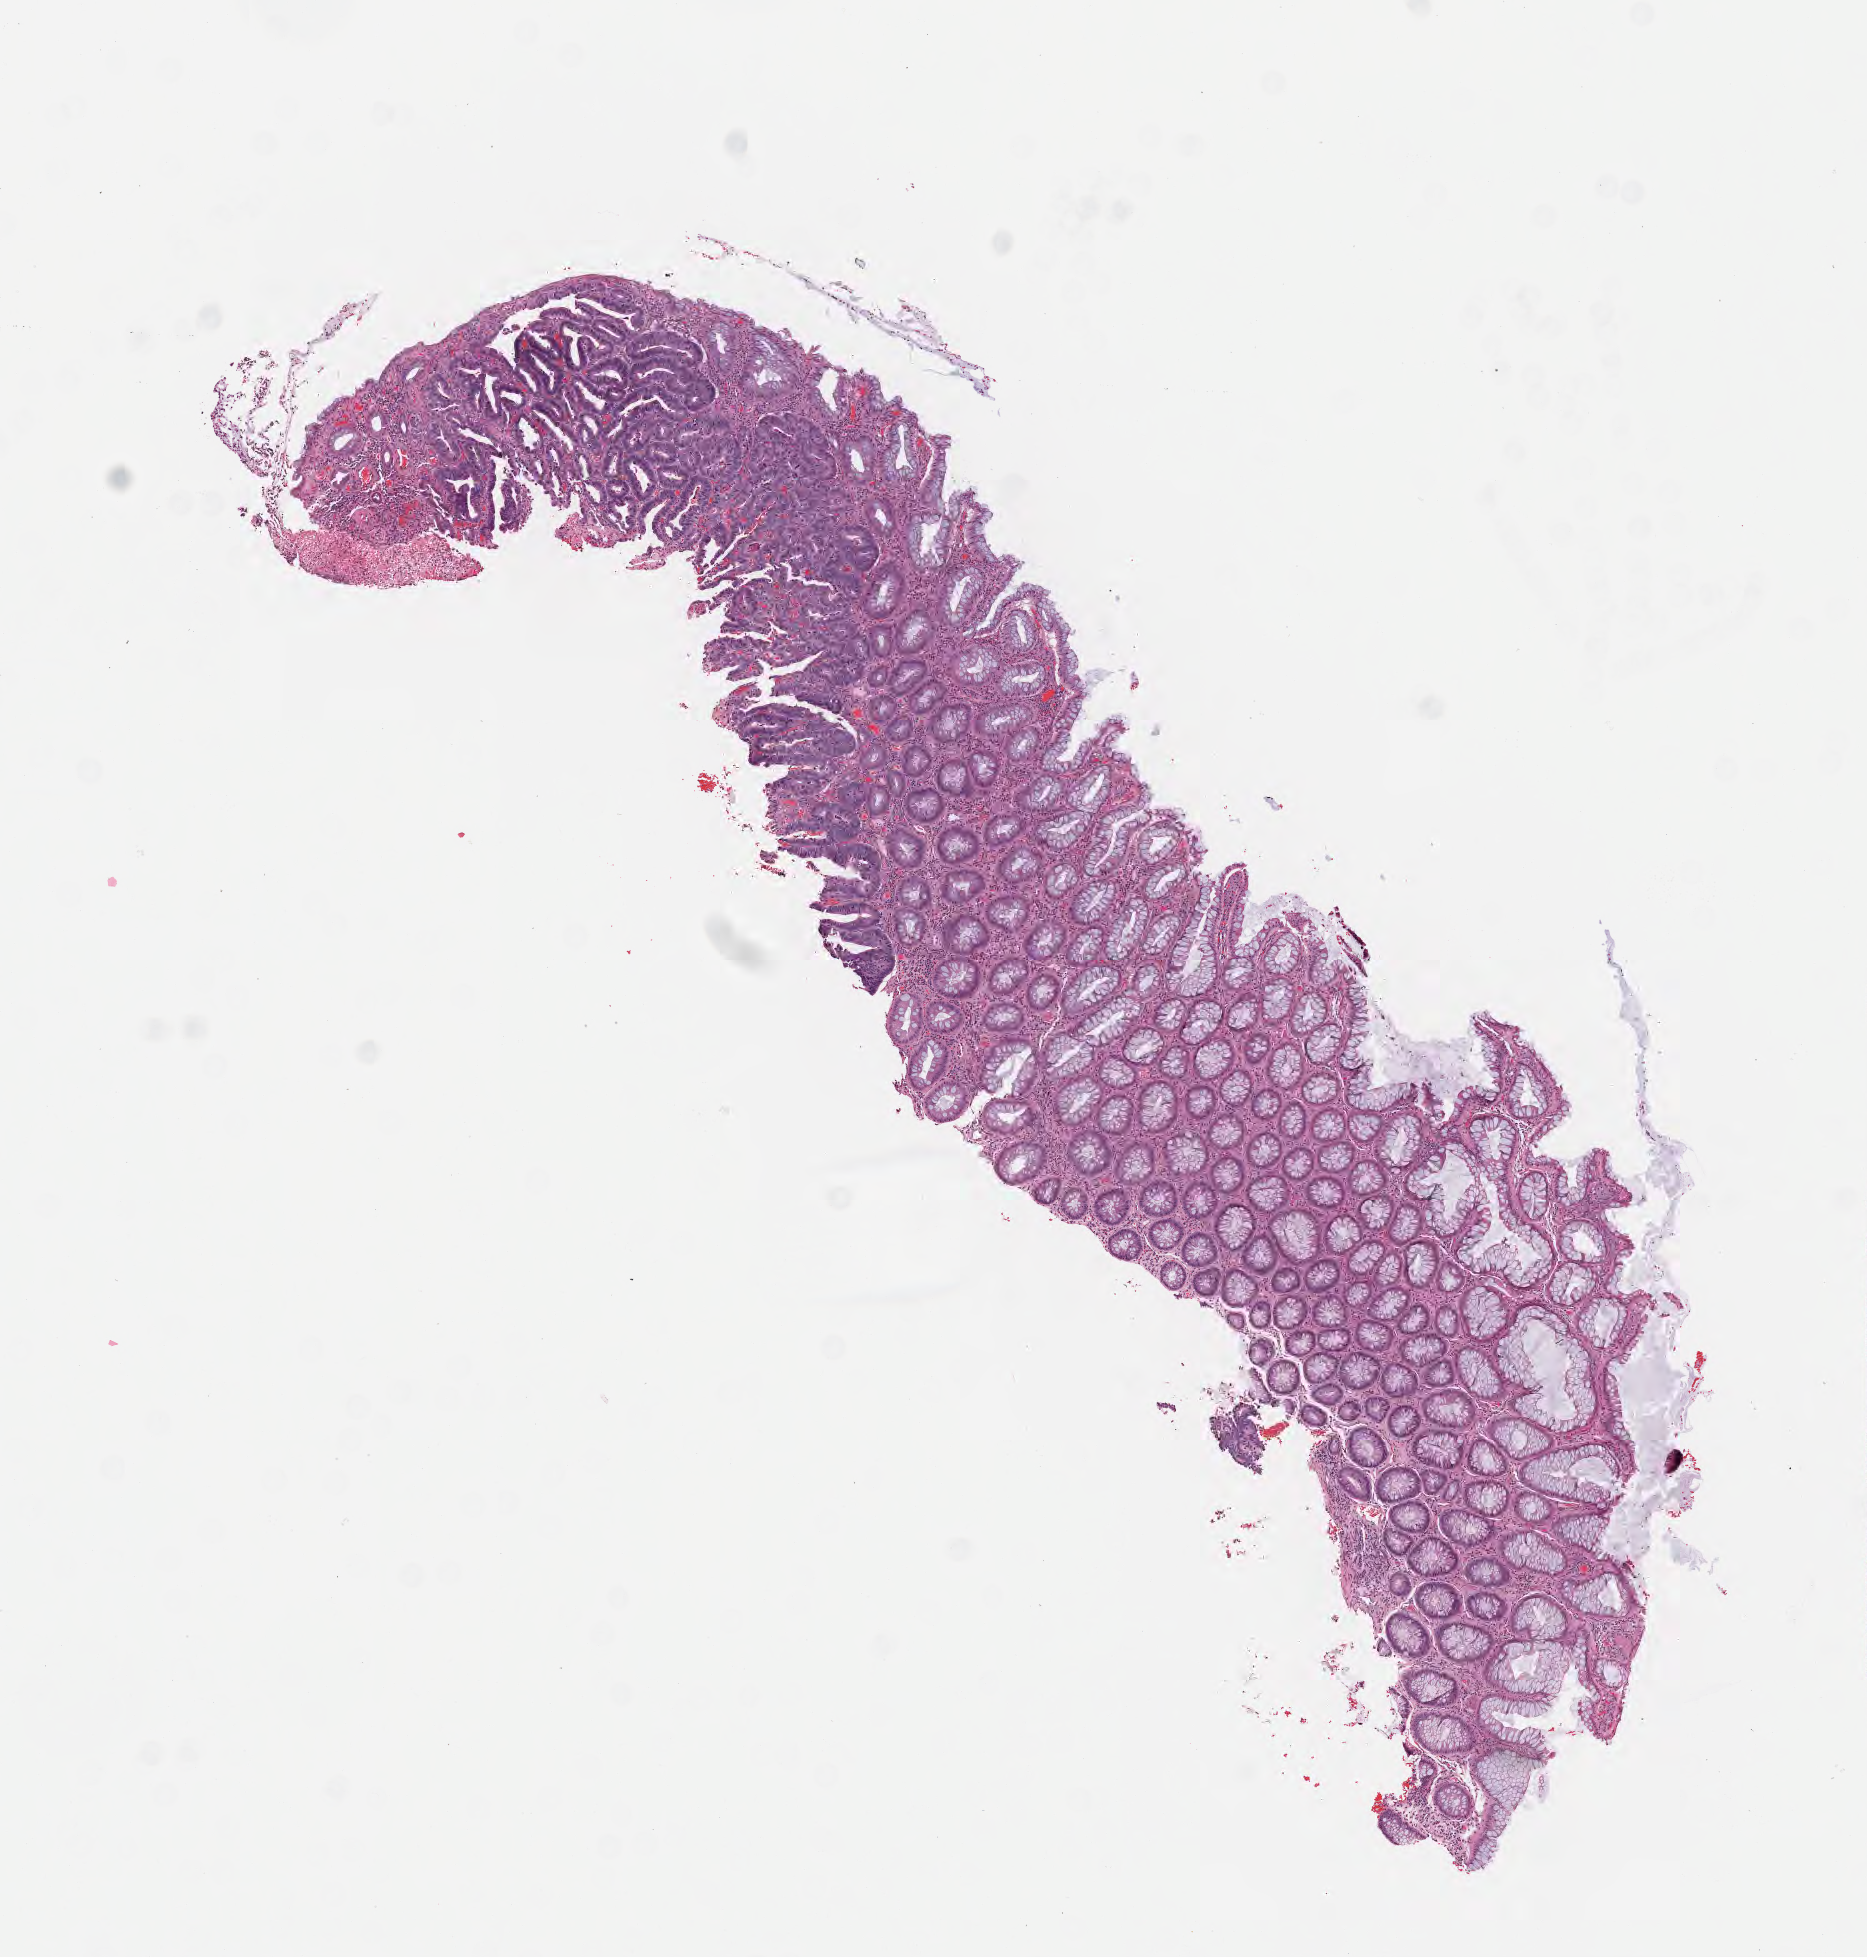
Digitized haematoxylin and eosin-stained section, low-resolution overview of the scanned area, about 7.5 x 7.9 mm, formalin-fixed paraffin-embedded section, primary tumor, anatomic site: sigmoid colon. Male patient; age at initial diagnosis 50 years. Tumor grade: G2 (moderately differentiated). Pathologist review of this section (percent, as recorded): tumor cells 50%, tumor nuclei 50%, stromal cells 24%, necrosis 1%, normal cells 25%. Inflammatory infiltration, as recorded: lymphocyte infiltration 7%, monocyte infiltration 3%, neutrophil infiltration 9%.
- section: bottom of the tissue portion
- diagnosis: Adenocarcinoma, NOS
- AJCC pathologic stage: Stage IIIB